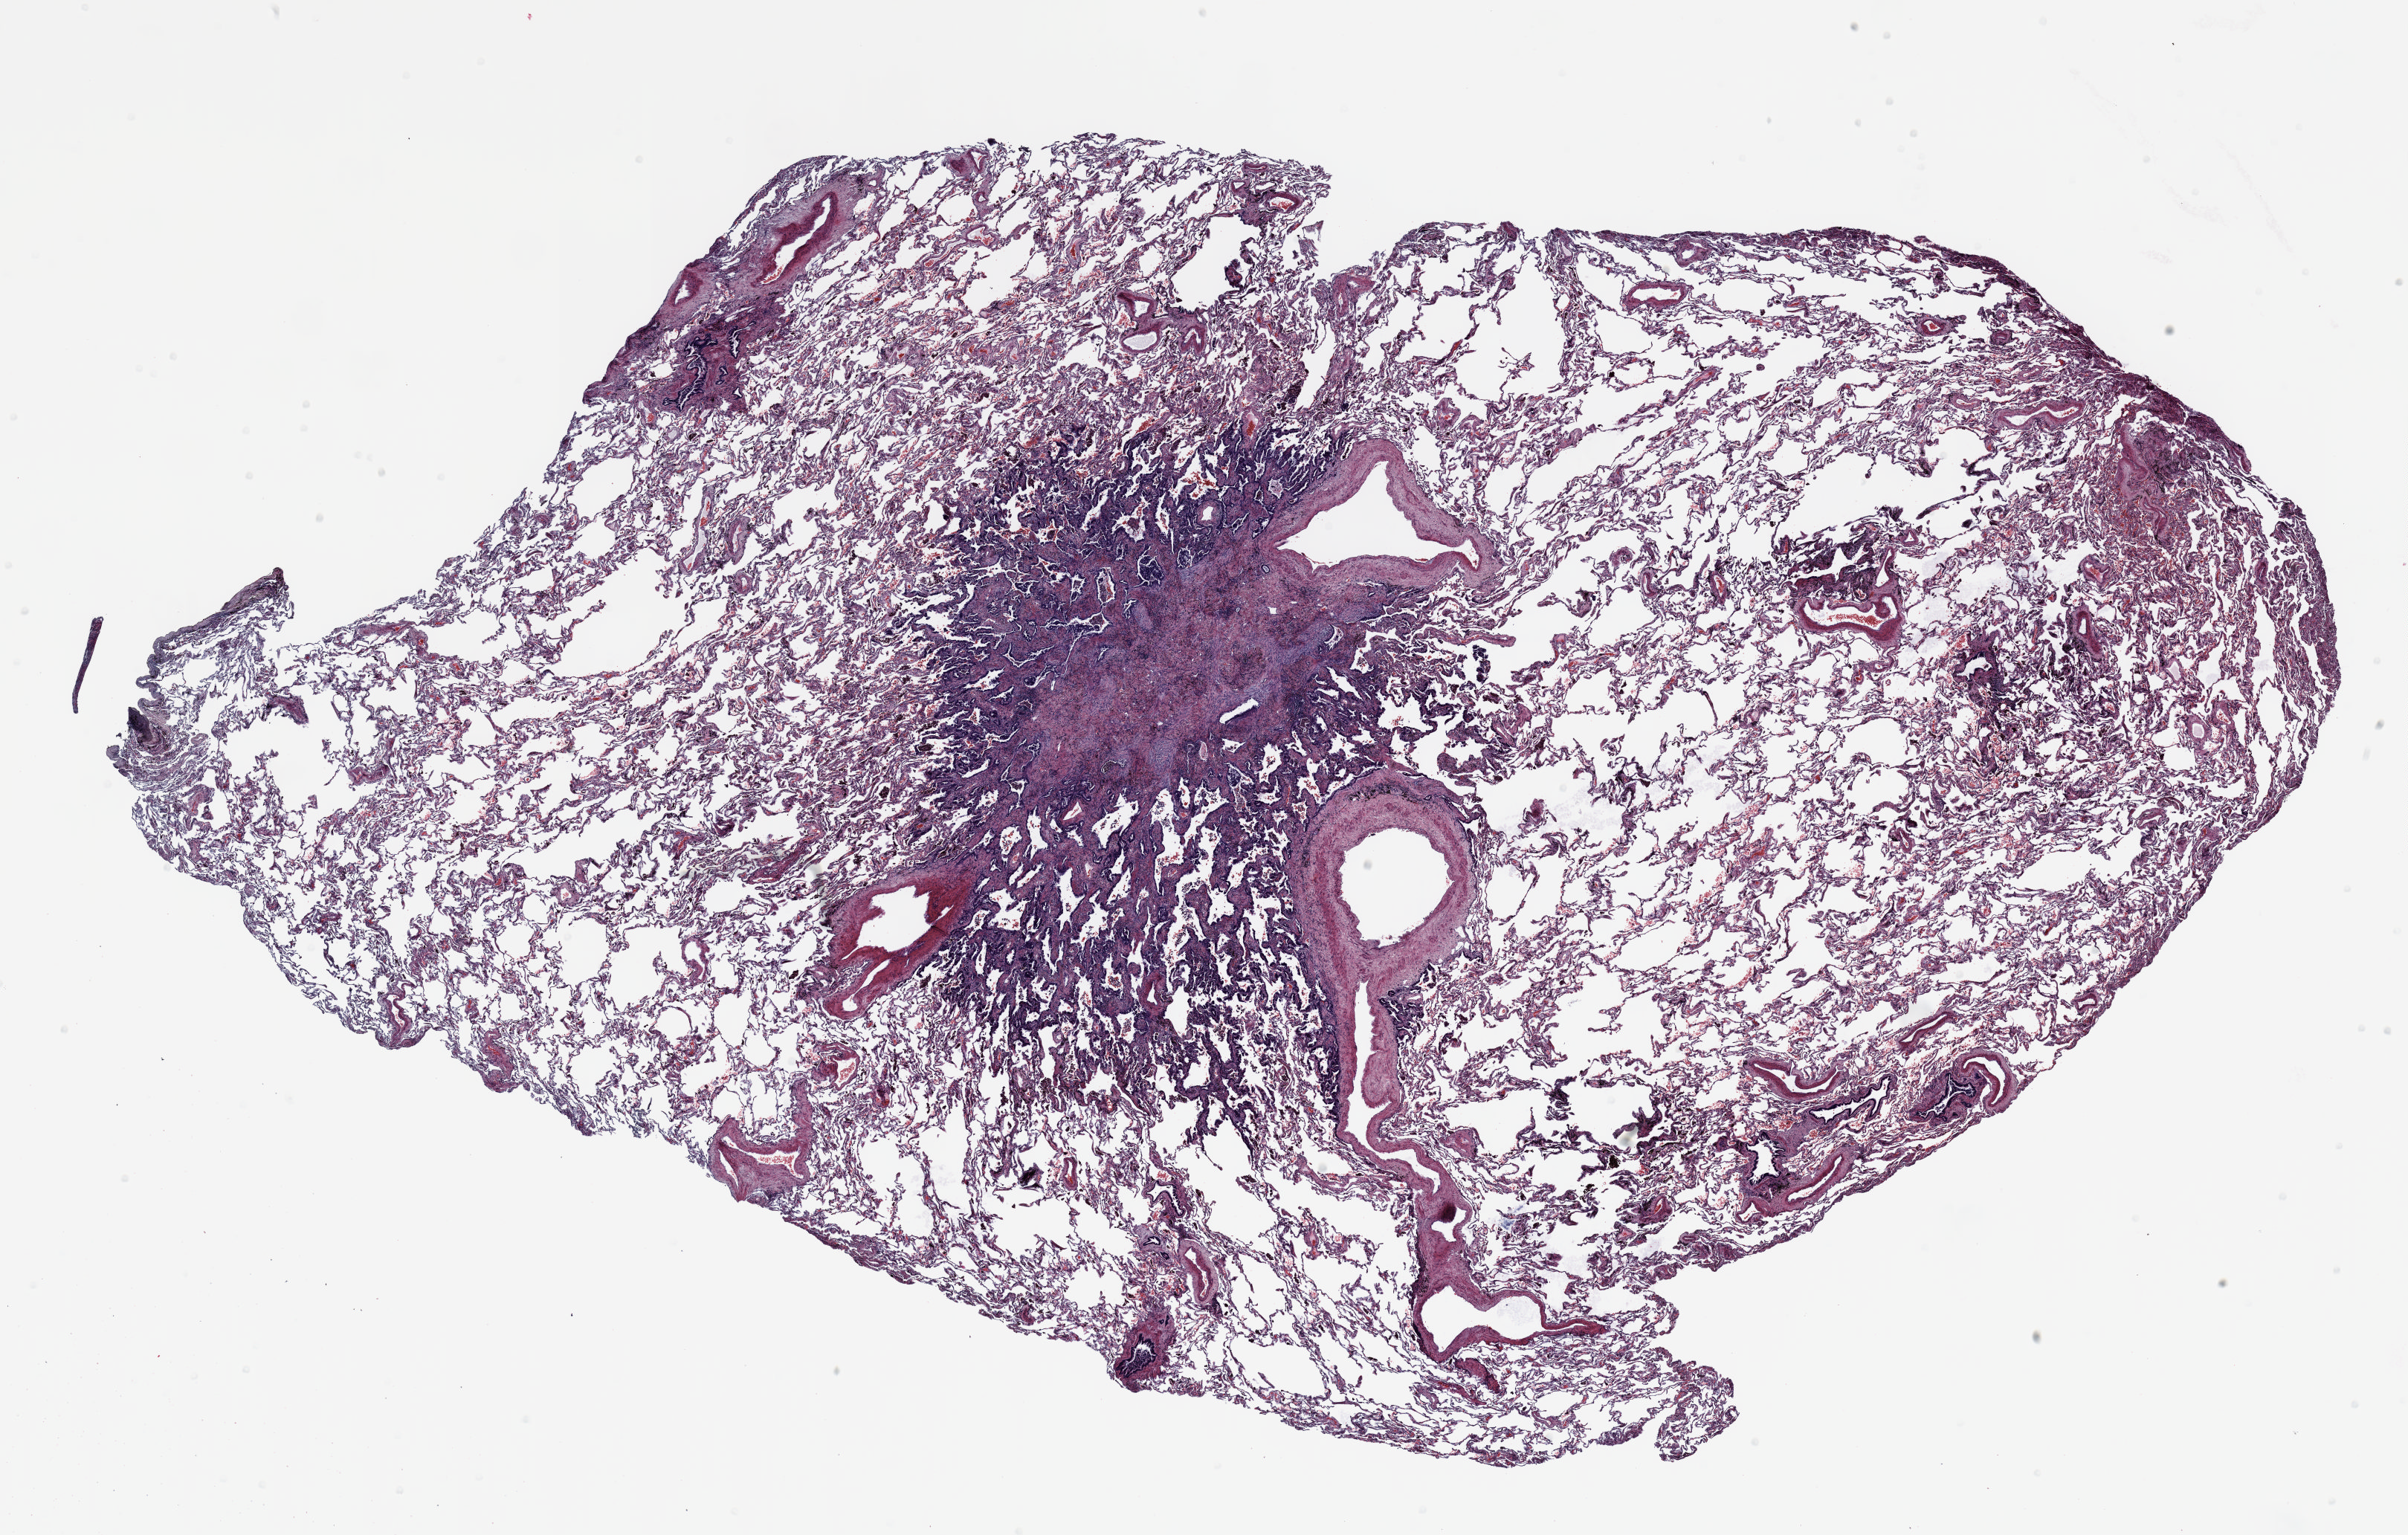
H&E whole-slide image — shown as a low-resolution overview of the whole scanned area (about 26.0 x 16.6 mm, acquisition: 20x scan). Formalin-fixed paraffin-embedded (FFPE) section. Lung. Male, age 69 at enrolment.
Participant's lung-cancer diagnosis: Mucinous adenocarcinoma.